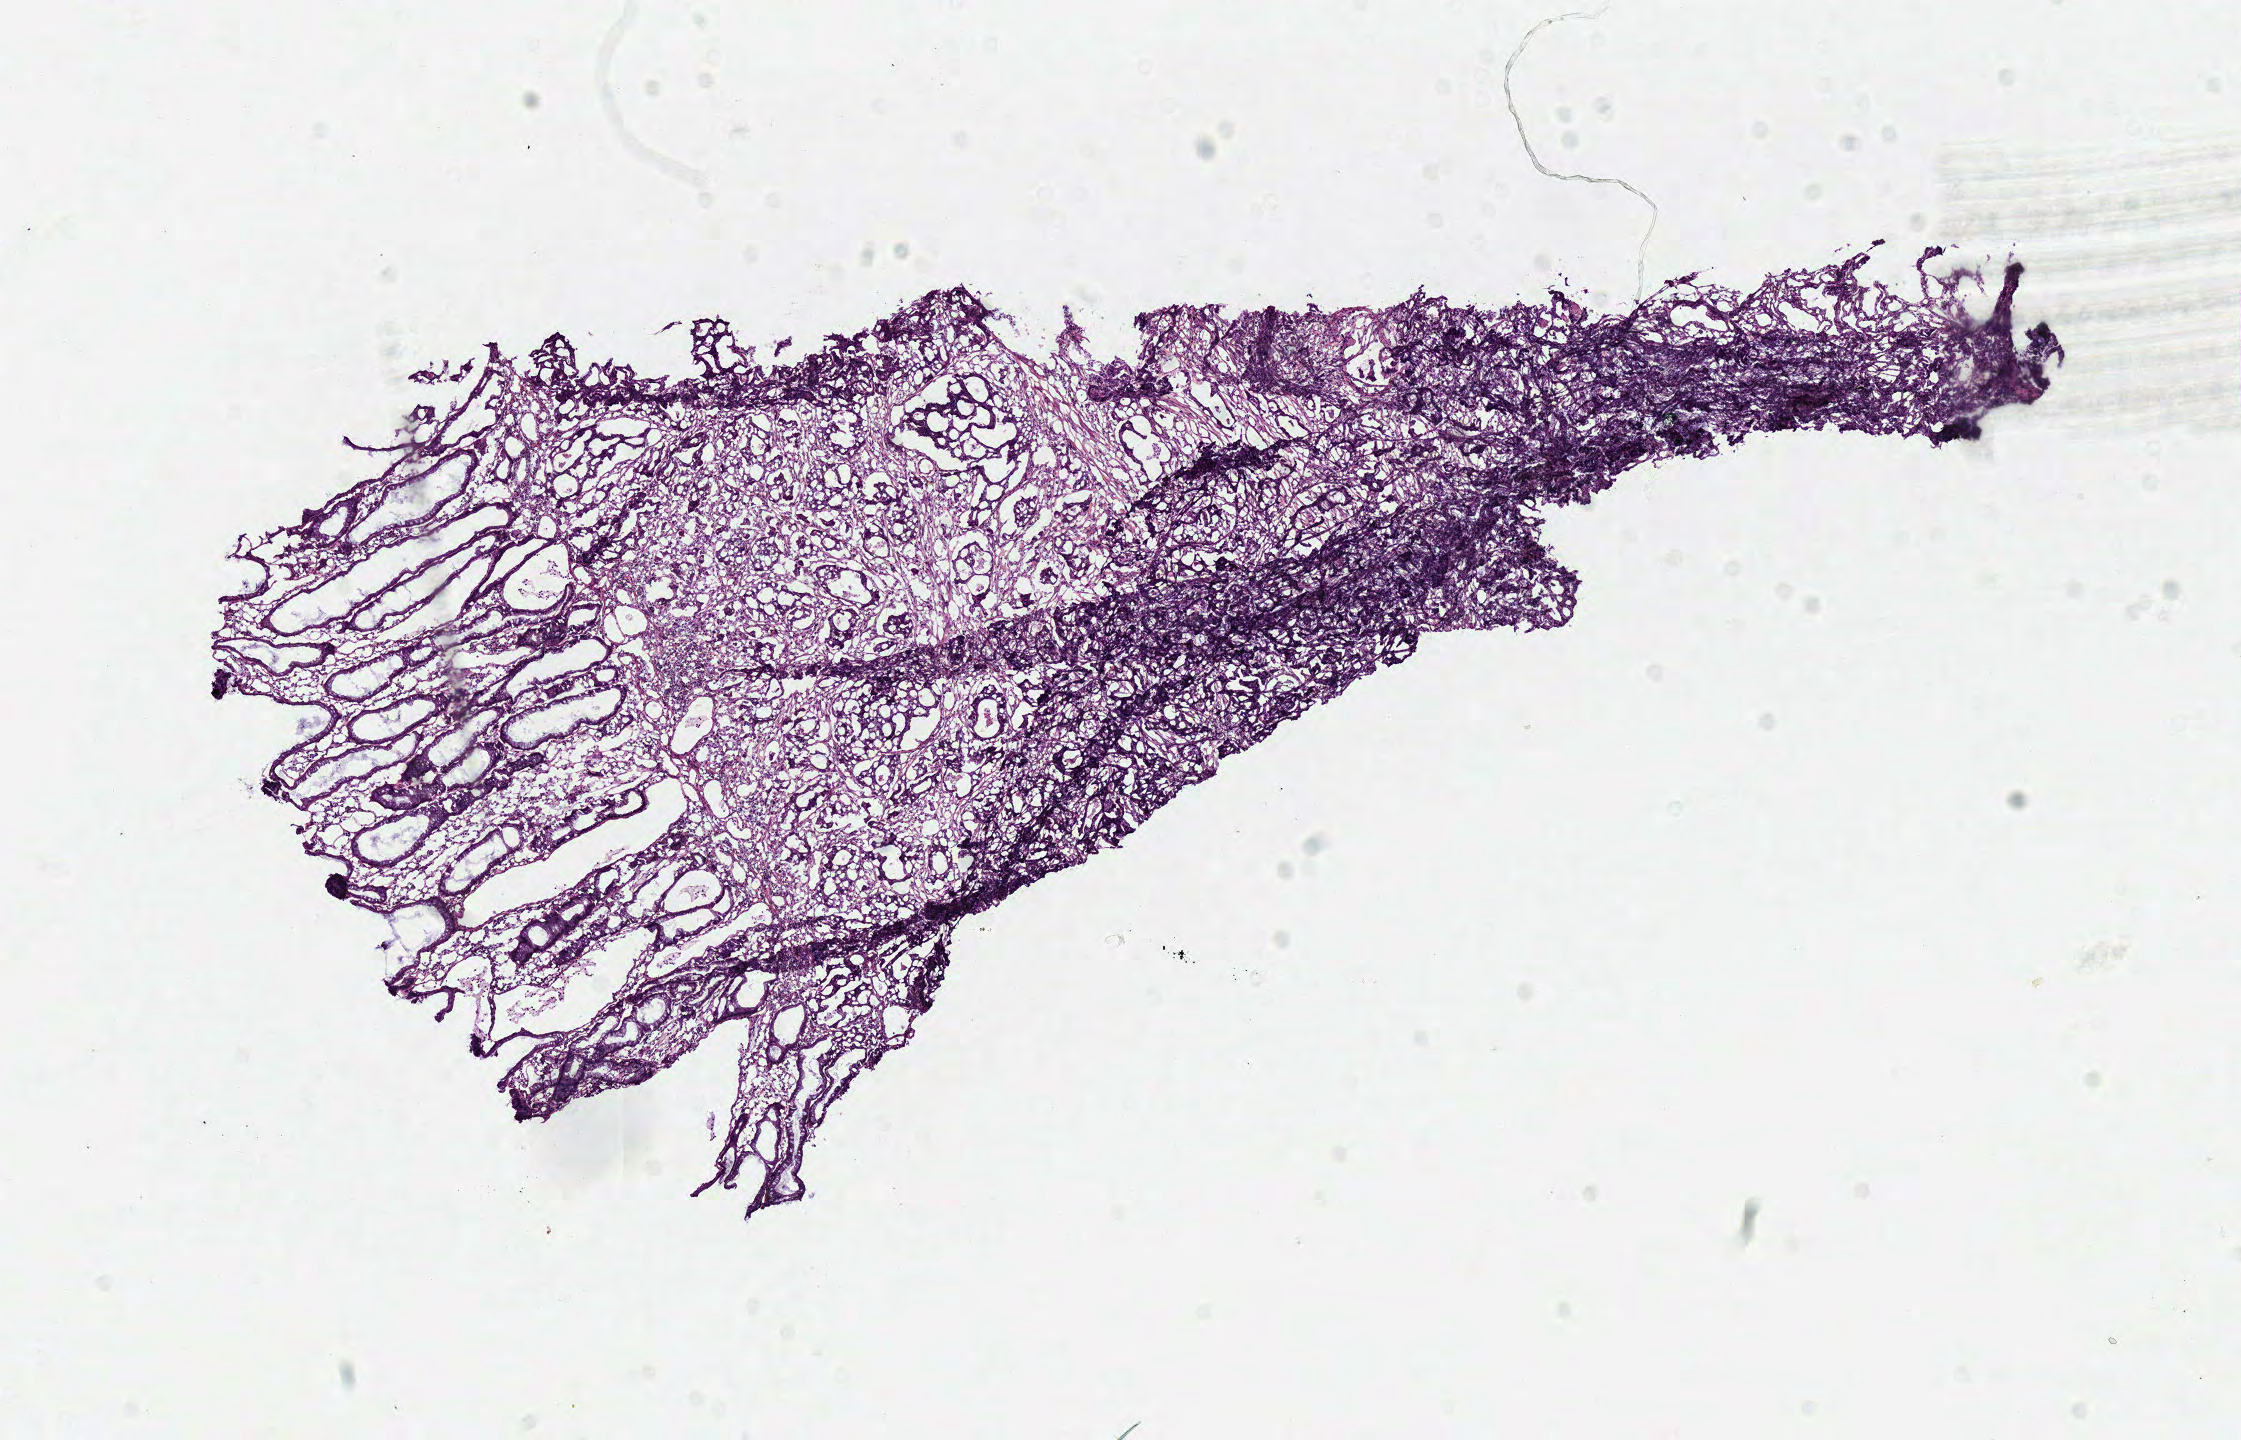
Whole-slide histology image, Hematoxylin and eosin (H&E) stained — whole scanned area (about 8.8 x 5.7 mm) shown as a low-resolution overview. Frozen section. Primary tumour sample from the colon. Patient: female, age at initial diagnosis 51 years. Slide review estimates, as recorded: tumour cells 55%, tumour nuclei 70%, normal cells 25%, stromal cells 15%, necrosis 5%.
Histologic diagnosis: Adenocarcinoma, NOS (sigmoid colon). Lymph nodes positive (case pathology): 6 of 109 examined. TNM: T3 N2 MX. AJCC pathologic stage: IIIC.